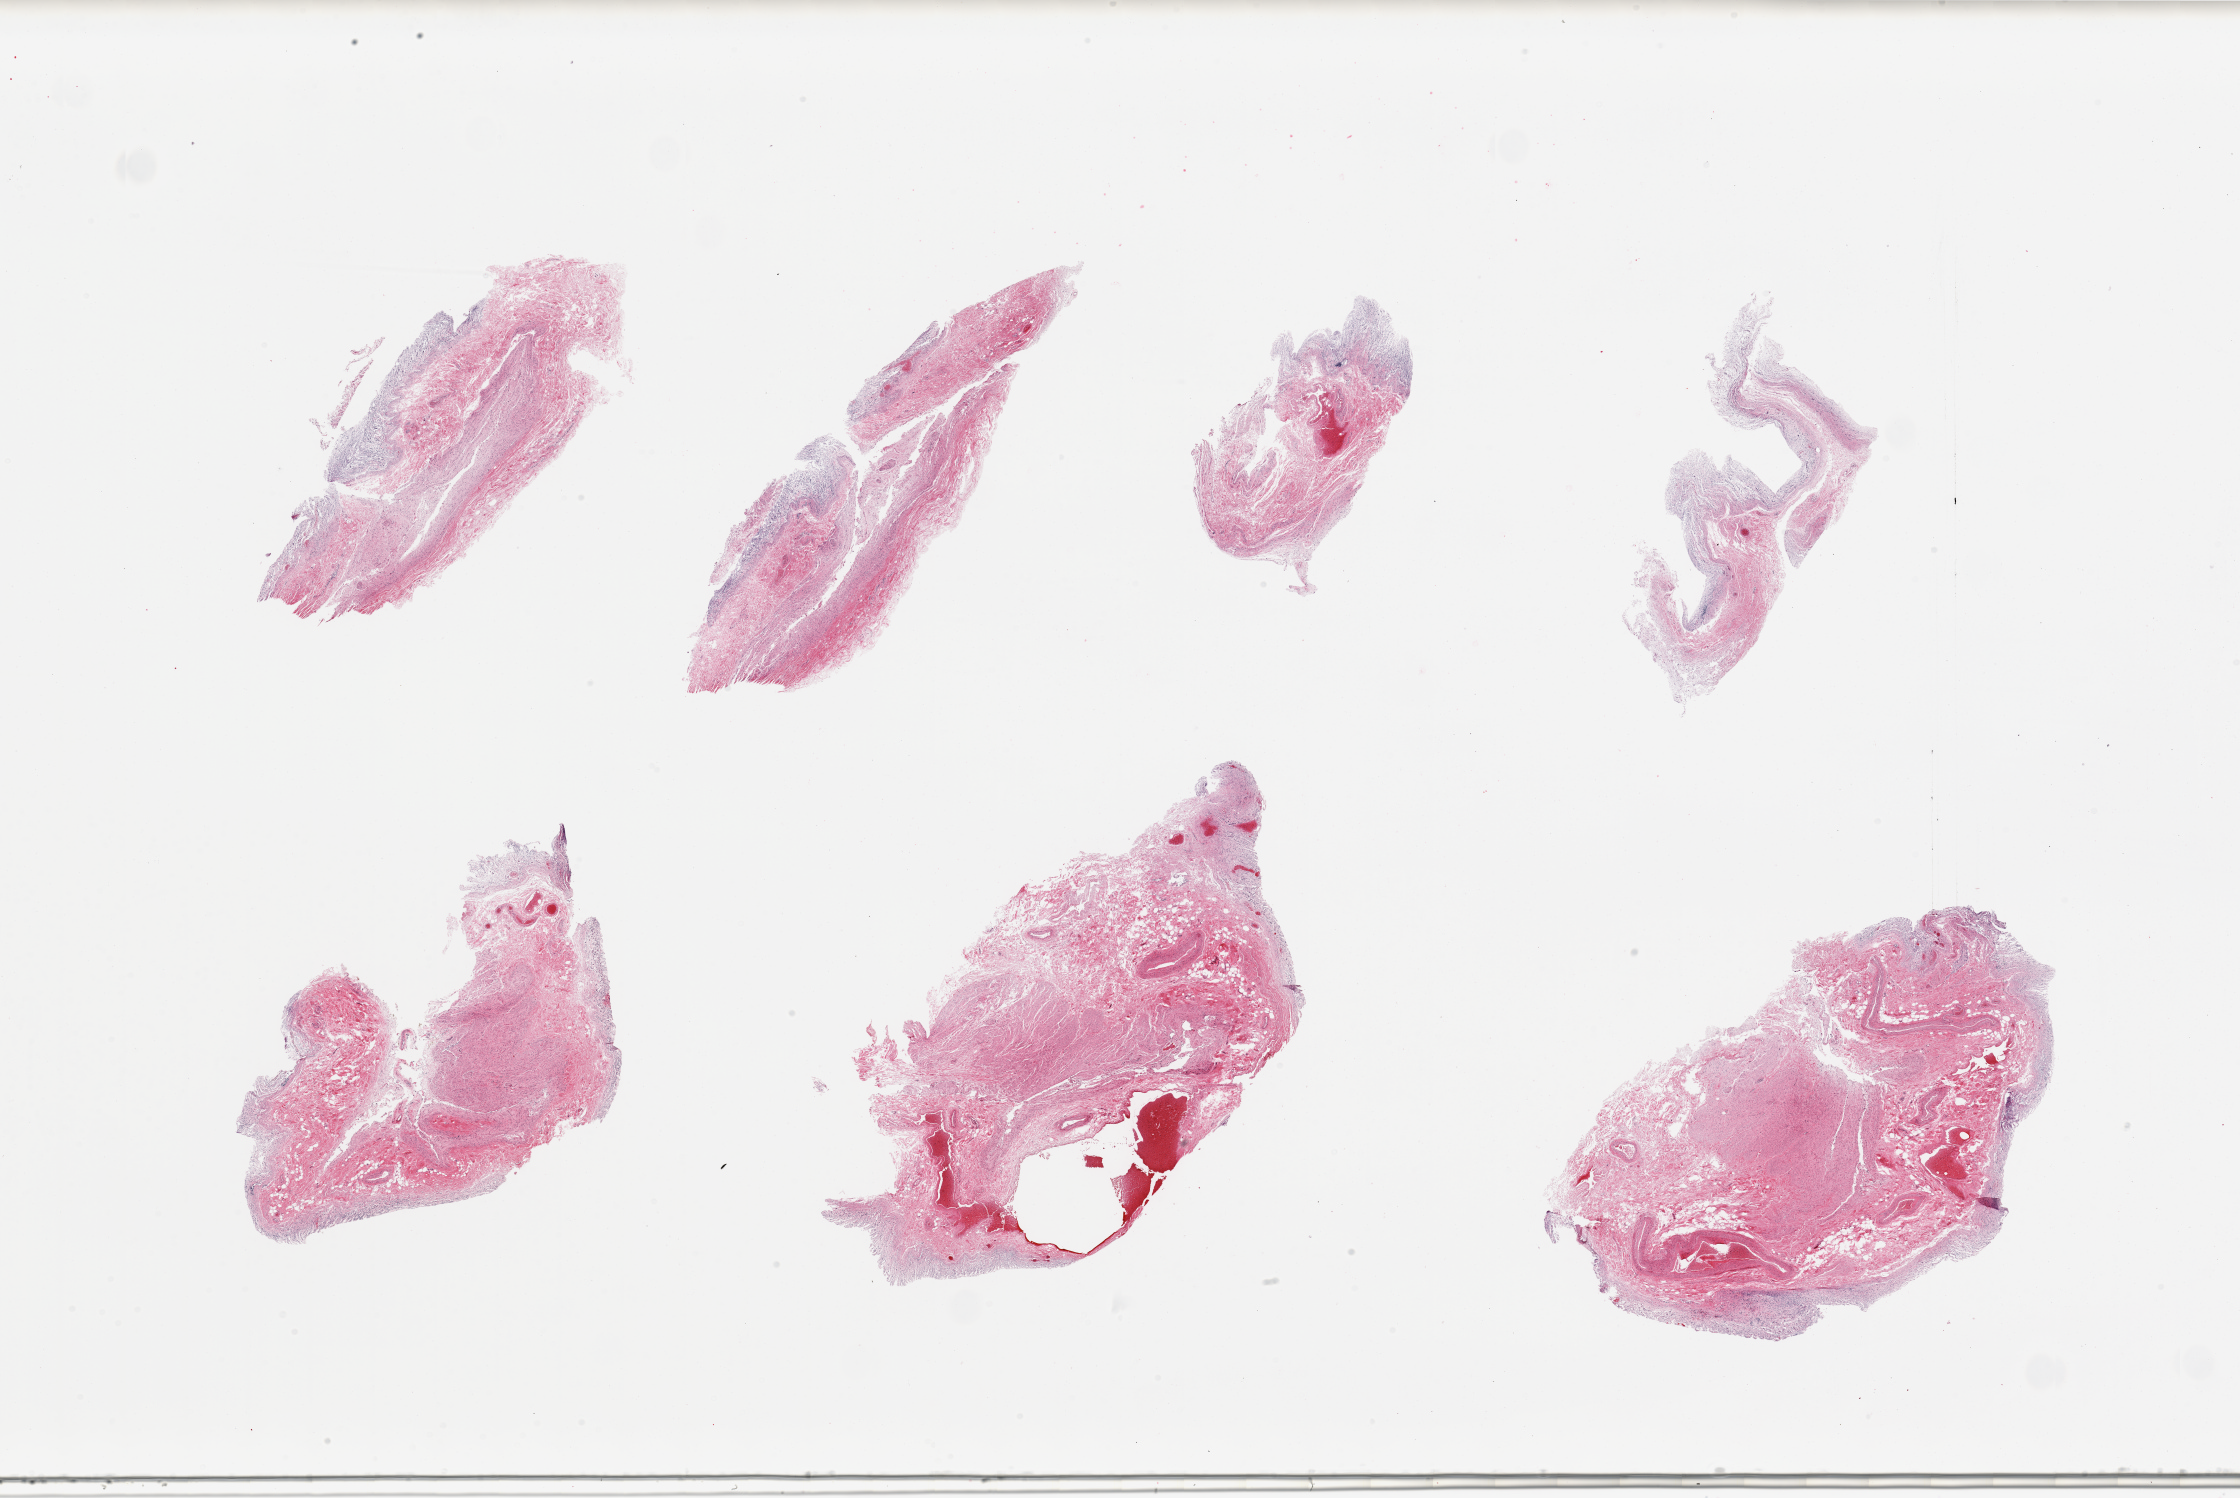
Whole-slide image, hematoxylin and eosin (H&E) stain — shown as a low-resolution overview of the whole scanned area (about 35.4 x 23.7 mm). PAXgene-fixed, paraffin-embedded tissue. Section of stomach (target tissue). Tissue donor sample.
Reviewer comment on this tissue sample: 6 pieces; autolyzed mucosa and muscularis.